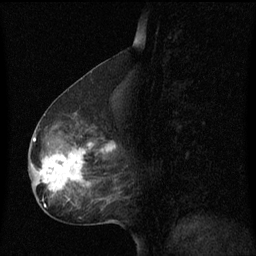
Breast MRI (dynamic contrast-enhanced), one sagittal slice. Position 33 of 60 along the scan axis. Dynamic contrast-enhanced series, image 2 of 3 at this slice position (ordered by acquisition). 1.5 T. TE 4.2 ms, TR 8.4 ms. 2 mm slice thickness. 256 × 256 image matrix. Female patient, age 49 years. From the clinical record (not read from this slice): setting: breast cancer imaged before/during neoadjuvant chemotherapy; receptor status: HR-positive, HER2-negative.
Outlined on this slice (semi-automatically segmented with operator editing):
- analysis volume of interest (the breast-tissue region the enhancement analysis was run in; not a lesion): bounding box (x1, y1, x2, y2) in pixels: (29, 126, 119, 201)
- tumour enhancement mask (voxels above the 70 % enhancement threshold inside the analysis volume of interest): (34, 138, 114, 193)